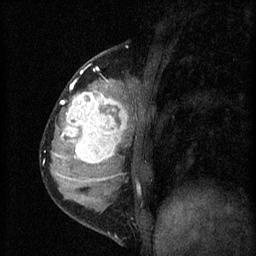
Breast MRI (dynamic contrast-enhanced), one sagittal slice. Slice 19 of 60 in the series (ordered by position). 3 images stored at this slice position (order not interpretable as contrast timing). 1.5 T. TE 4.2 ms, TR 8.2 ms. 256 × 256 image matrix. Patient: female, 37 years.
Outlined on this slice (semi-automatically segmented with operator editing):
- analysis volume of interest (the breast-tissue region the enhancement analysis was run in; not a lesion): bounding box [x1, y1, x2, y2] px = [53, 78, 140, 181]
- tumour enhancement mask (voxels above the 70 % enhancement threshold inside the analysis volume of interest): [61, 80, 128, 181]